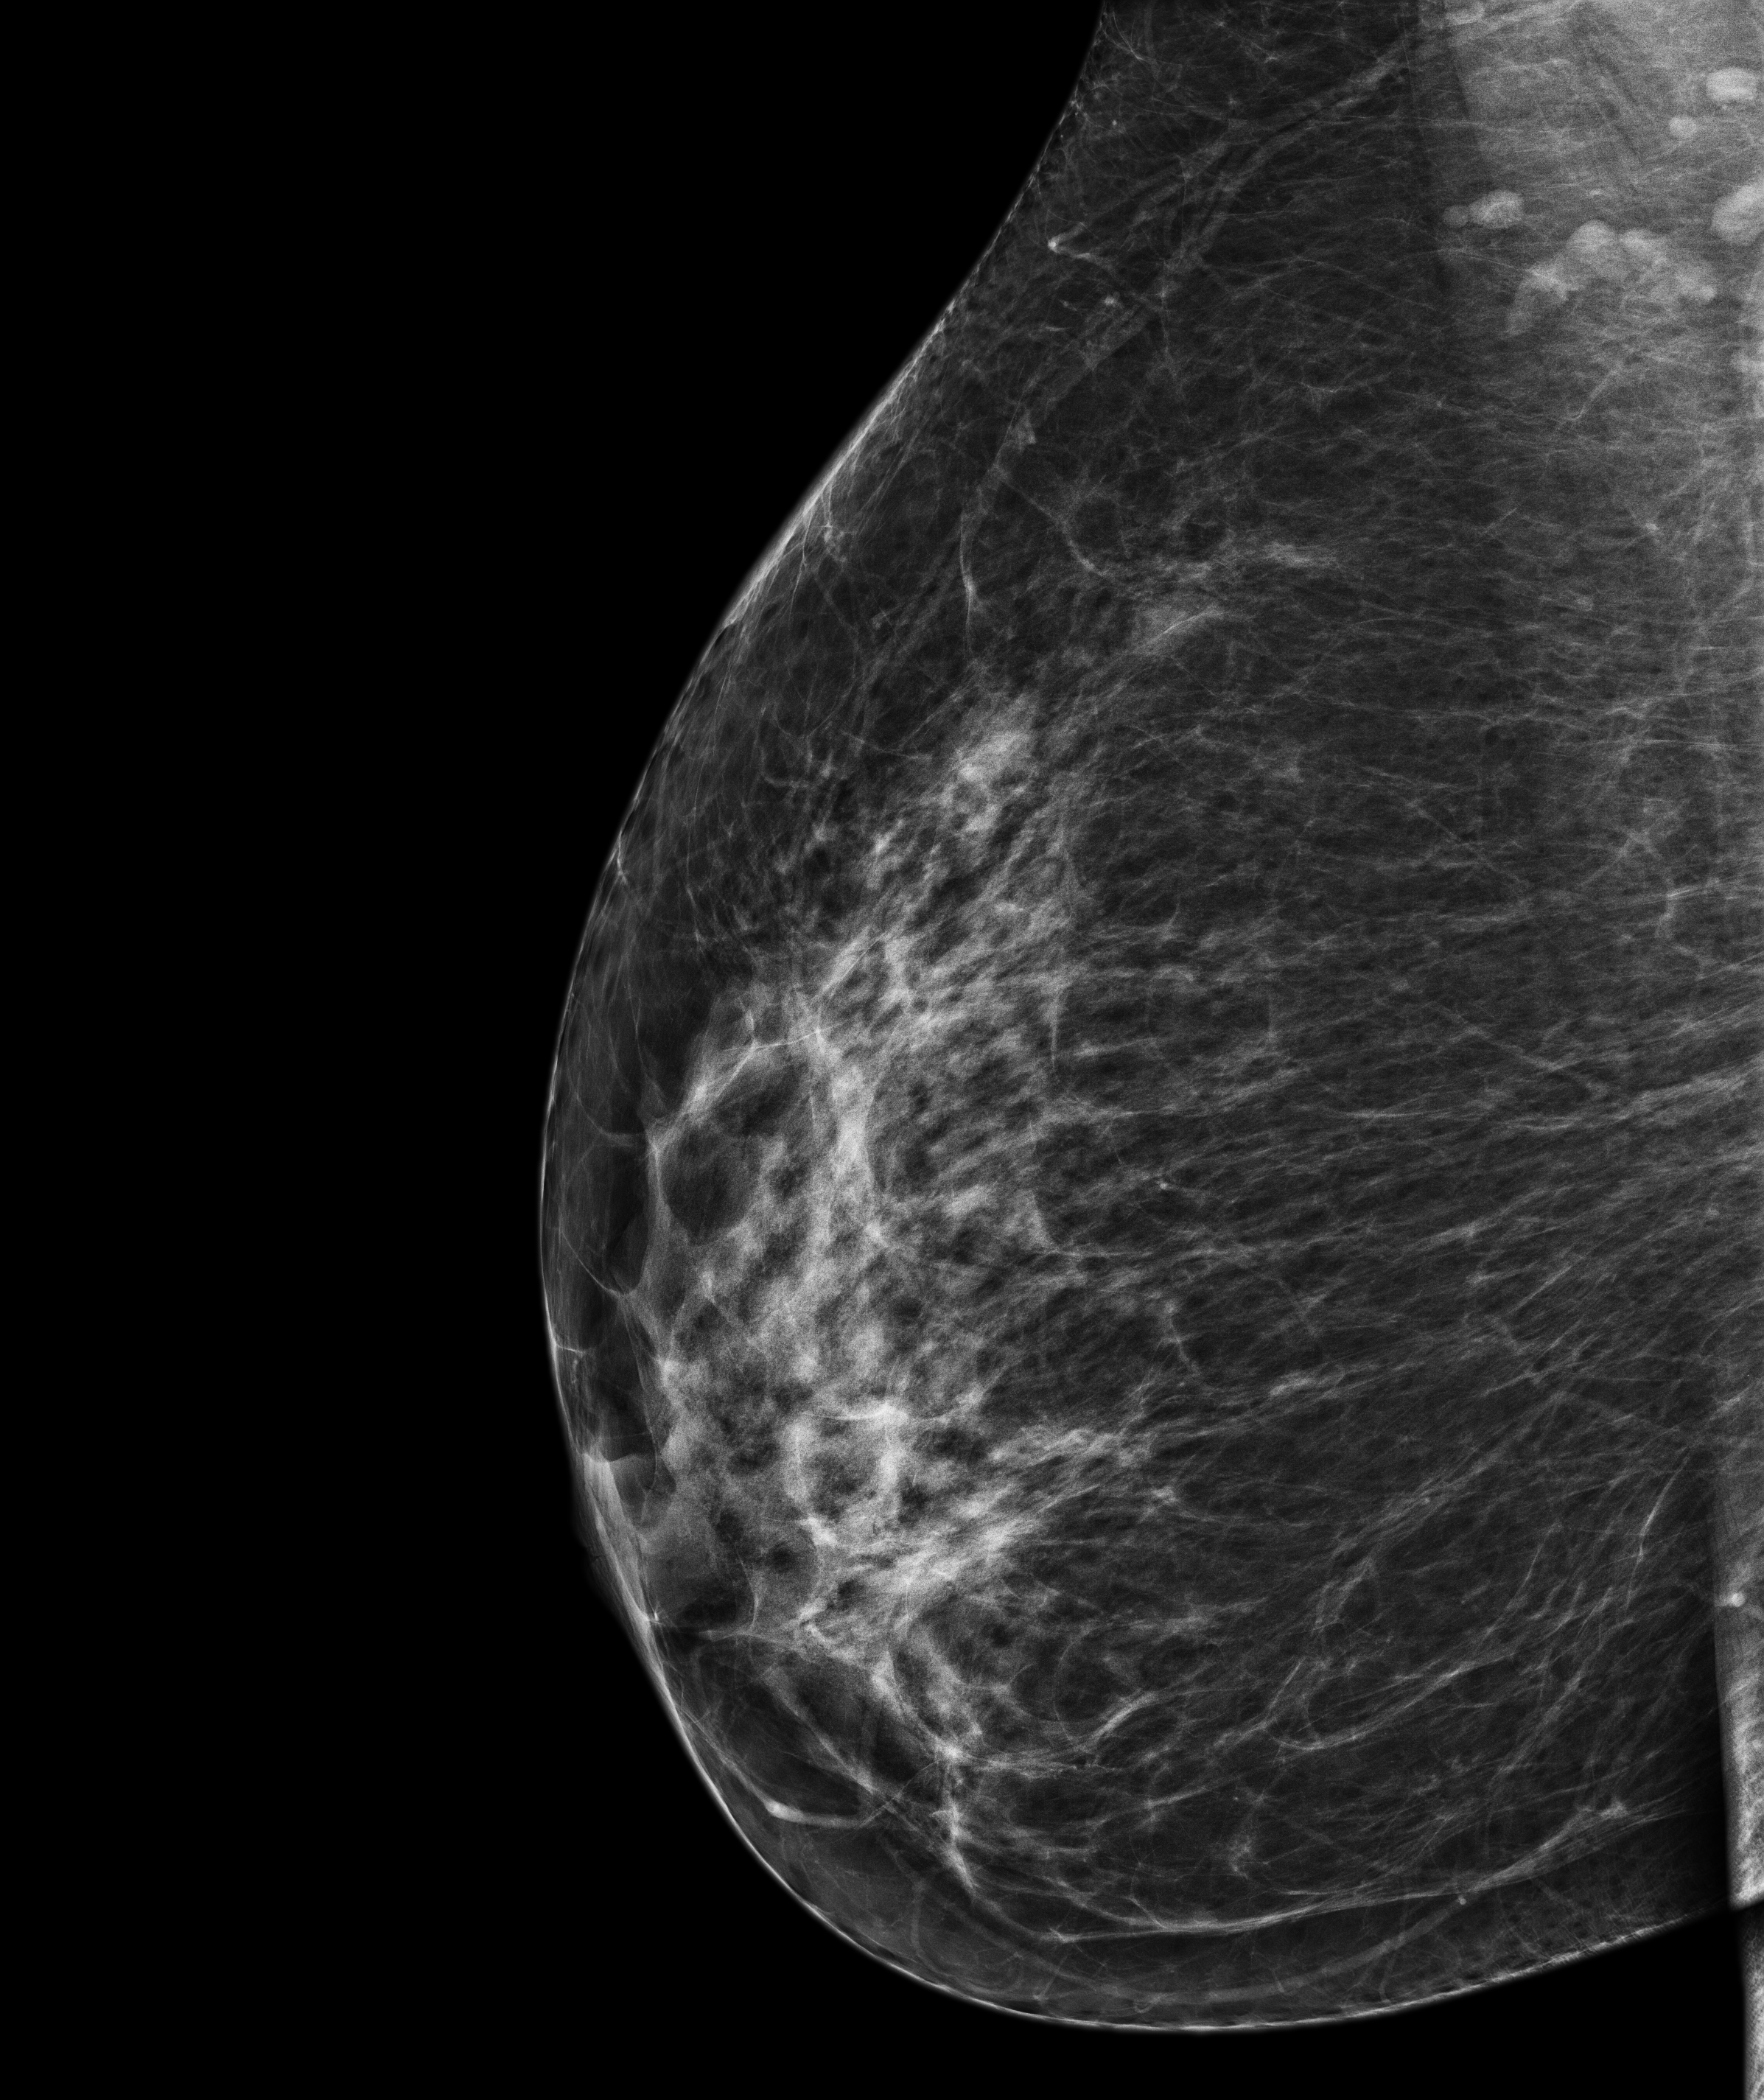
Screening examination. Patient aged 57 years (female).
Image type: full-field digital mammogram. Breast: right. Projection: MLO view.